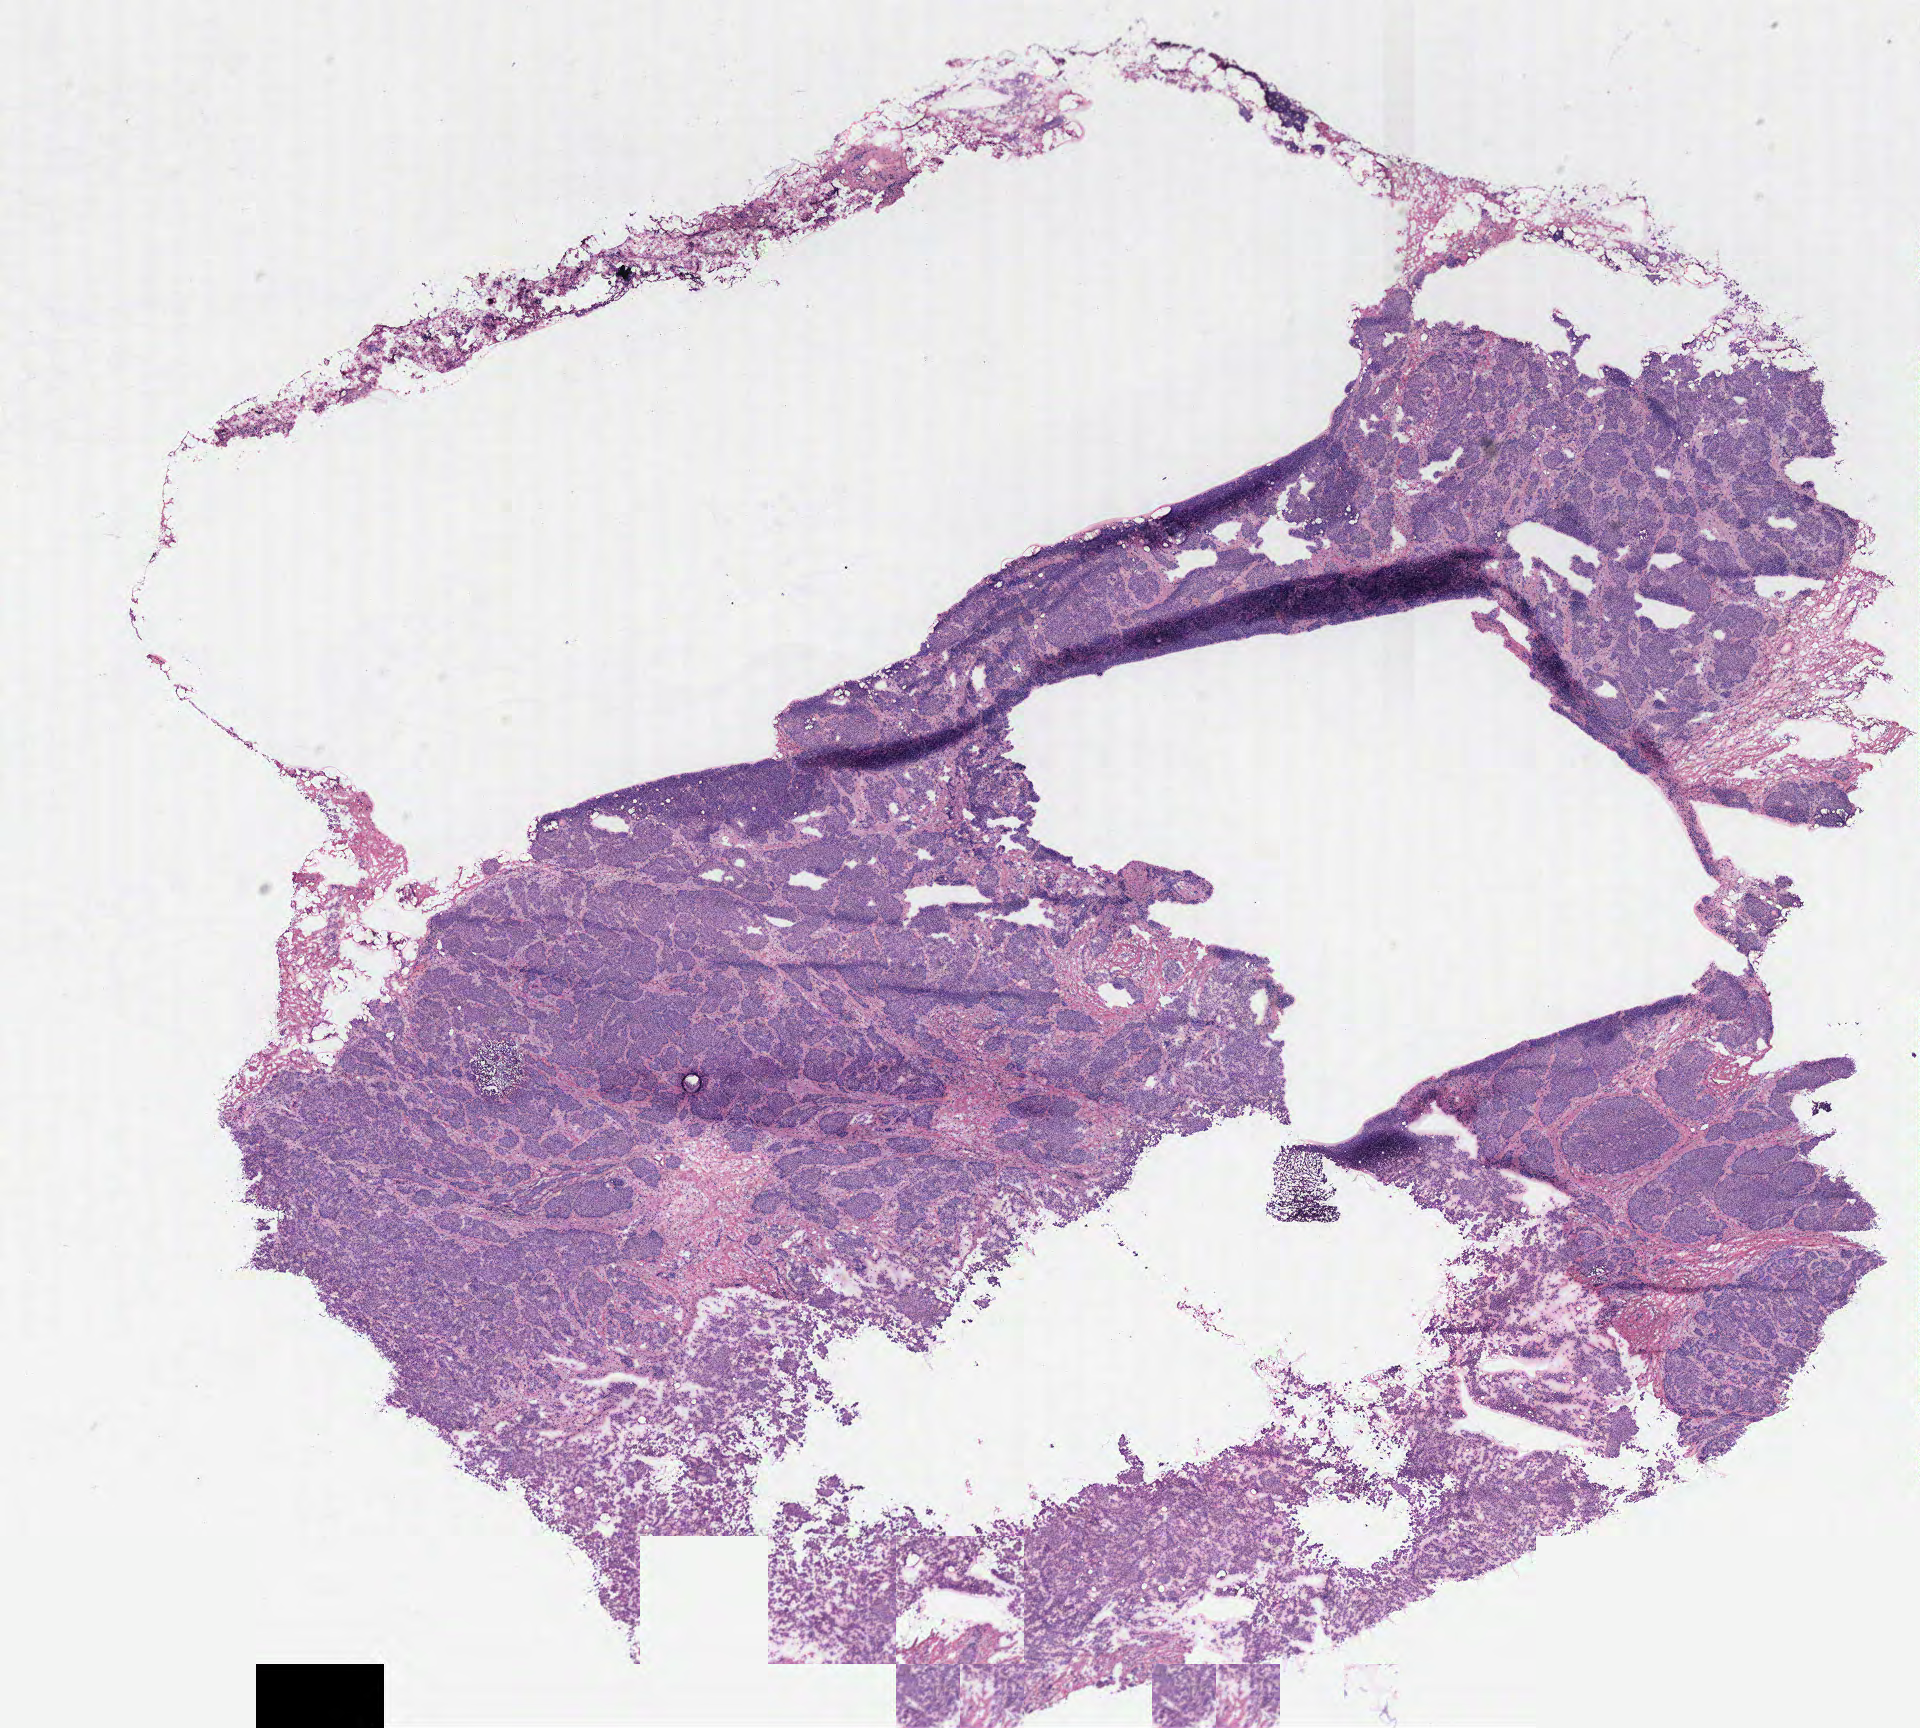
Hematoxylin and eosin (H&E) stained whole-slide image — whole scanned area (about 15.4 x 13.8 mm) shown as a low-resolution overview. Tumour tissue sample, breast. Female, 84 y/o.
* diagnosis: Infiltrating duct carcinoma, NOS
* AJCC pathologic stage: IIA